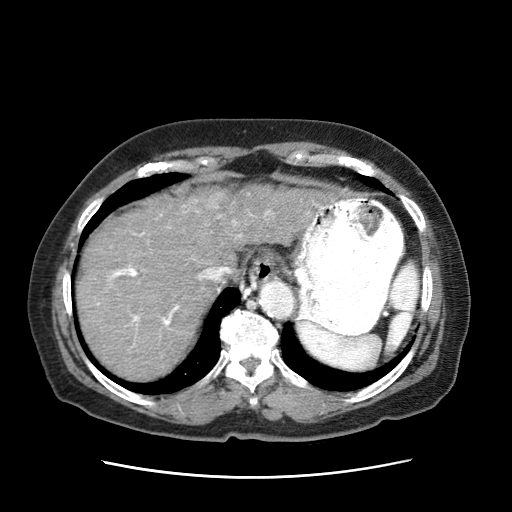
Contrast-enhanced abdominal CT (liver protocol), one axial slice. Position 55 of 63 along the scan axis. Reconstruction kernel STANDARD. 120 kVp. Intravenous contrast given. Soft-tissue window (W 400 / L 40 HU). 2.5 mm slice thickness. 512 × 512 image matrix, field of view 360 × 360 mm. Female patient, age 79 years. Case-level facts recorded for this patient, not image findings: diagnosis: hepatocellular carcinoma (patient treated with transarterial chemoembolisation; whether this scan precedes or follows treatment is not stated here); TNM stage (as recorded): Stage-II; Child-Pugh class: B; tumour differentiation: well differentiated; tumour nodularity: multinodular.
Outlined on this slice (semi-automatically segmented with operator editing):
- abdominal aorta: box from (x=259, y=282) to (x=295, y=320) px
- liver parenchyma outside the tumour (the mass and vessels are separate outlines, so this box may not span the whole liver): (x=78, y=194)–(x=237, y=384)
- mass: (x=181, y=184)–(x=335, y=256)
- liver vessels: (x=94, y=212)–(x=245, y=327)